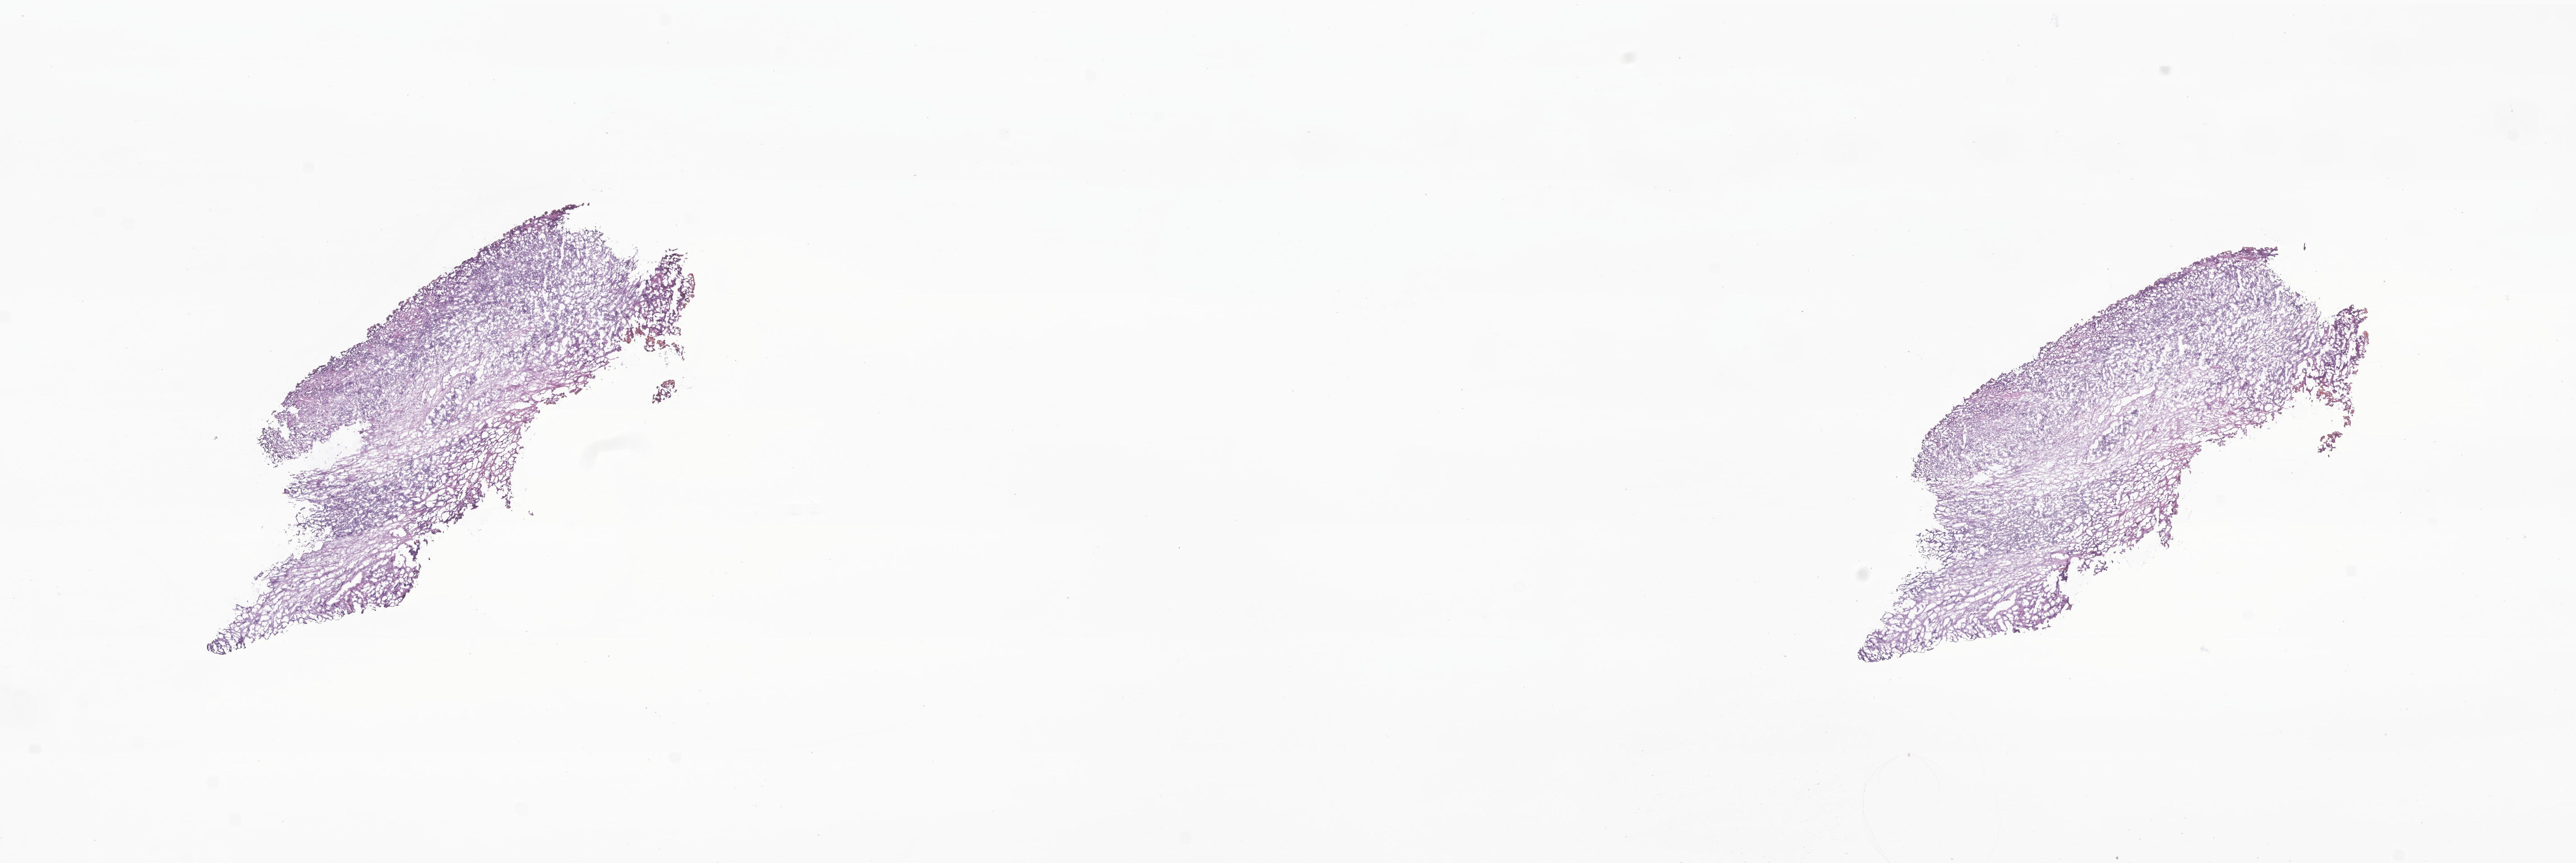
Digitized H&E-stained section of tumor tissue from the prostate — whole scanned area (about 24.0 x 8.1 mm) shown as a low-resolution overview; frozen section. Male patient, age 210 months (17 years 6 months).
Recorded diagnosis: Rhabdomyosarcoma, NOS.